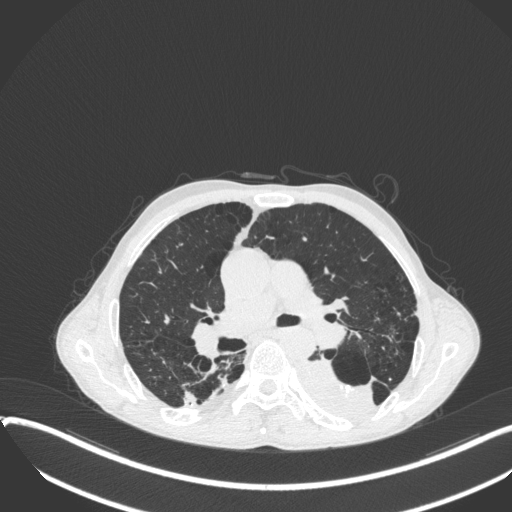
Chest CT, one axial slice; slice 228 of 400 in the series (ordered by position); 120 kVp; lung window (W 1500 / L -600 HU); 1 mm slice thickness; 512 × 512 image matrix, field of view 400 × 400 mm. Patient: male, 57 years. Case-level facts recorded for this patient, not image findings: clinical TNM (as recorded): T4 N0 M0.
Annotated regions visible in this slice (bounding box drawn by a radiologist):
- lung tumour (recorded histology: squamous cell carcinoma): bounding box (x1, y1, x2, y2) in pixels: (294, 353, 376, 423)